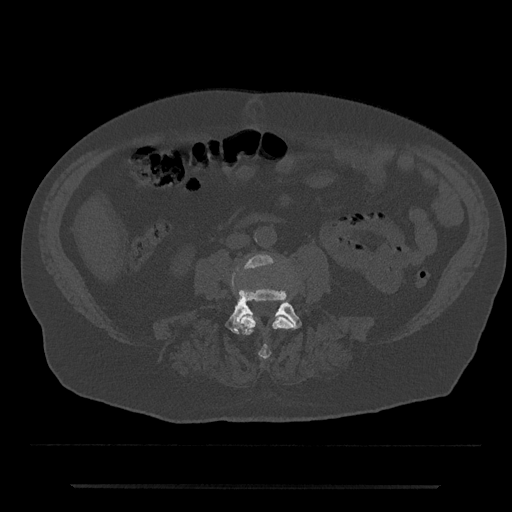
CT including the spine, one axial slice; position 374 of 797 along the scan axis; reconstruction kernel Br40s/3; 120 kVp; bone window (W 1800 / L 400 HU); 0.5 mm slice thickness; 512 × 512 image matrix. Male patient, age 80 years. Case-level facts recorded for this patient, not image findings: primary cancer: prostate.
Outlined on this slice (semi-automatically segmented with operator editing):
- L3 vertebra: bounding box (x1, y1, x2, y2) in pixels: (232, 255, 294, 359)
- L4 vertebra: (211, 288, 302, 334)